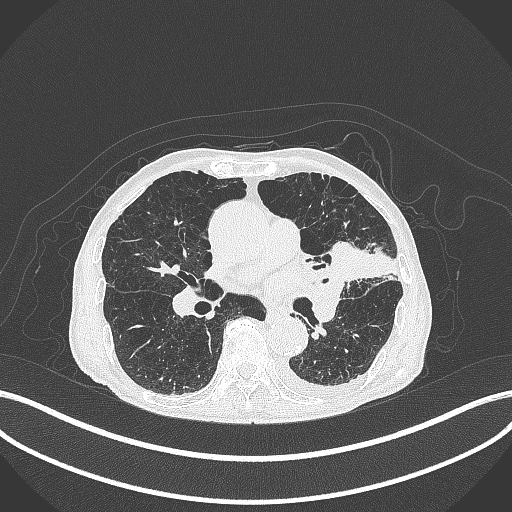
Chest CT, one axial slice; reconstruction kernel B70f; lung window (W 1500 / L -600 HU); 1 mm slice thickness; 512 × 512 image matrix, field of view 400 × 400 mm. Patient: male, 90 years or older. Case-level facts recorded for this patient, not image findings: clinical TNM (as recorded): T2b N1 M0.
Outlined on this slice (bounding box drawn by a radiologist):
- lung tumour (recorded histology: squamous cell carcinoma): bounding box <317,236,397,289> (left, top, right, bottom; pixels)